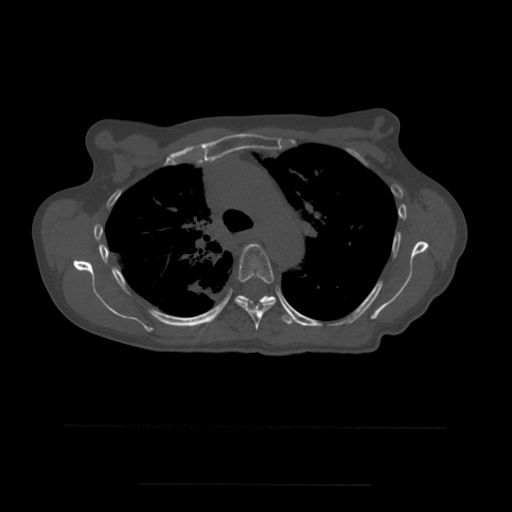
CT including the spine, one axial slice; slice 389 of 544 in the series (ordered by position); bone window (W 1800 / L 400 HU); 1.25 mm slice thickness; 512 × 512 image matrix, field of view 350 × 350 mm. Patient age 58 years. From the clinical record (not read from this slice): primary cancer: lung.
Annotated regions visible in this slice (semi-automatically segmented with operator editing):
- T4 vertebra: bounding box <250,244,255,247> (left, top, right, bottom; pixels)
- T5 vertebra: <235,244,276,330>
- T6 vertebra: <235,295,295,325>